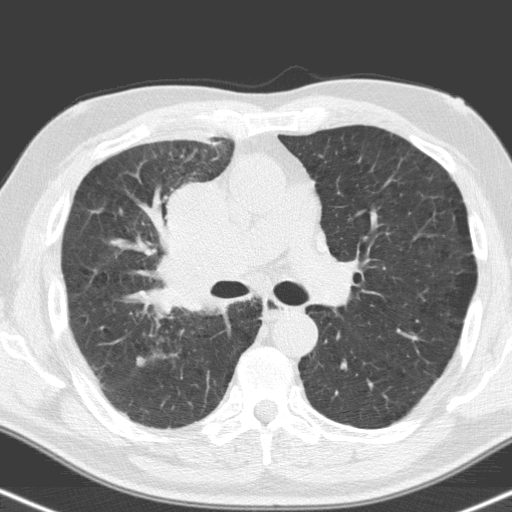
Low-dose screening chest CT, one axial slice. Position 100 of 160 along the scan axis. 120 kVp. Lung window (W 1500 / L -600 HU). 3.2 mm slice thickness. 512 × 512 image matrix.
Annotated regions visible in this slice (expert manual segmentation):
- lesion 1 (tumor, hilum of right lung): bounding box <160,184,253,312> (left, top, right, bottom; pixels)